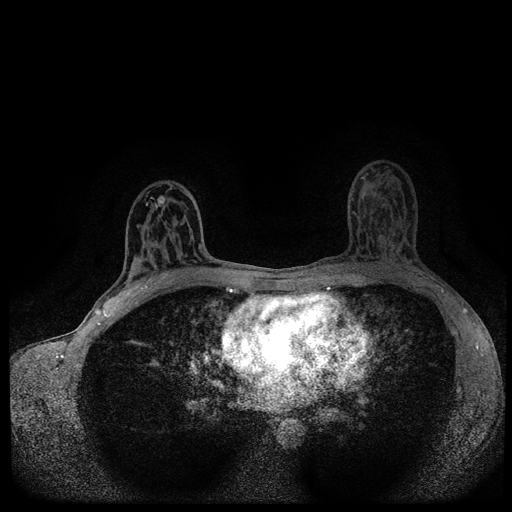
Breast MRI (dynamic contrast-enhanced, multi-phase), one axial slice; dynamic contrast-enhanced series, time point 2 of 5 at this slice position (early post-contrast); 1.5 T; TE 2.7 ms, TR 5.4 ms; 2 mm slice thickness; 512 × 512 image matrix. Female patient, age 43 years.
Annotated regions visible in this slice (semi-automatically segmented with operator editing):
- breast lesion (labelled 'tumour' in the annotation; benign lesions carry a separate 'benign' label): box from (x=157, y=194) to (x=166, y=207) px